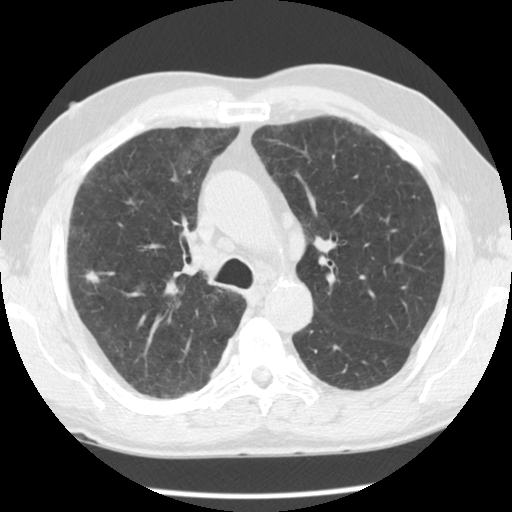
Low-dose screening chest CT, one axial slice; reconstruction kernel STANDARD; lung window (W 1500 / L -600 HU); 512 × 512 image matrix, field of view 330 × 330 mm.
Annotated regions visible in this slice (expert manual segmentation):
- lesion 2 (nodule): bounding box (x1, y1, x2, y2) in pixels: (85, 271, 100, 284)